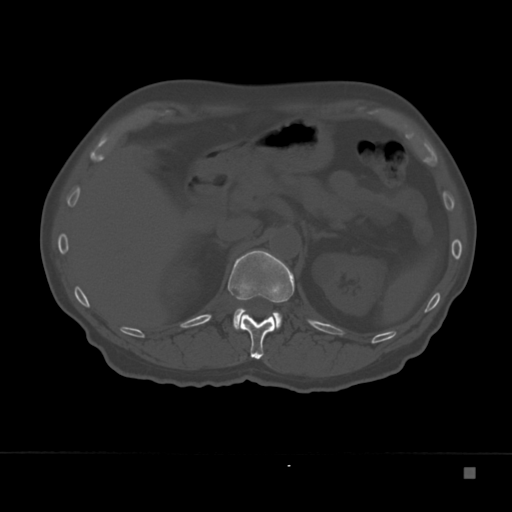
CT including the spine, one axial slice; position 125 of 332 along the scan axis; 120 kVp; bone window (W 1800 / L 400 HU); 512 × 512 image matrix, field of view 389 × 389 mm. Patient: male, 72 years. Case-level facts recorded for this patient, not image findings: primary cancer: skeletal.
Structures marked on this image (semi-automatically segmented with operator editing):
- L1 vertebra: bounding box <233,308,282,330> (left, top, right, bottom; pixels)
- T12 vertebra: <227,250,295,359>